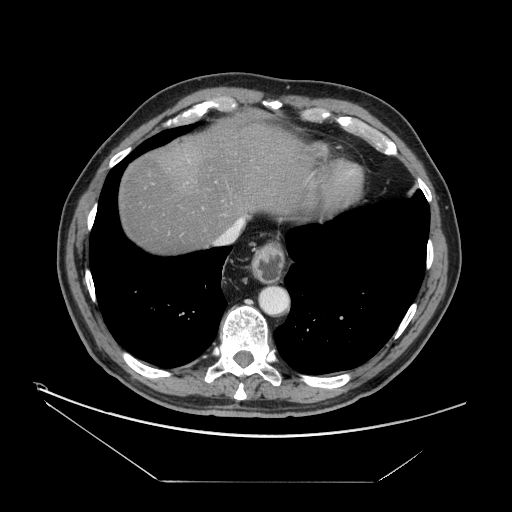
Contrast-enhanced abdominal CT, one axial slice; slice 141 of 161 in the series (ordered by position); reconstruction kernel STANDARD; intravenous contrast given; soft-tissue window (W 400 / L 40 HU); 2.5 mm slice thickness; 512 × 512 image matrix. Male patient, age 65 years. From the clinical record (not read from this slice): diagnosis: colorectal cancer liver metastases, imaged before liver resection; multiple liver metastases: yes; largest metastasis: 4.2 cm.
Annotated regions visible in this slice (expert manual segmentation):
- hepatic veins: bounding box (x1, y1, x2, y2) in pixels: (220, 218, 244, 244)
- liver: (118, 115, 310, 253)
- planned liver remnant (the part of the liver to remain after resection): (118, 116, 310, 253)